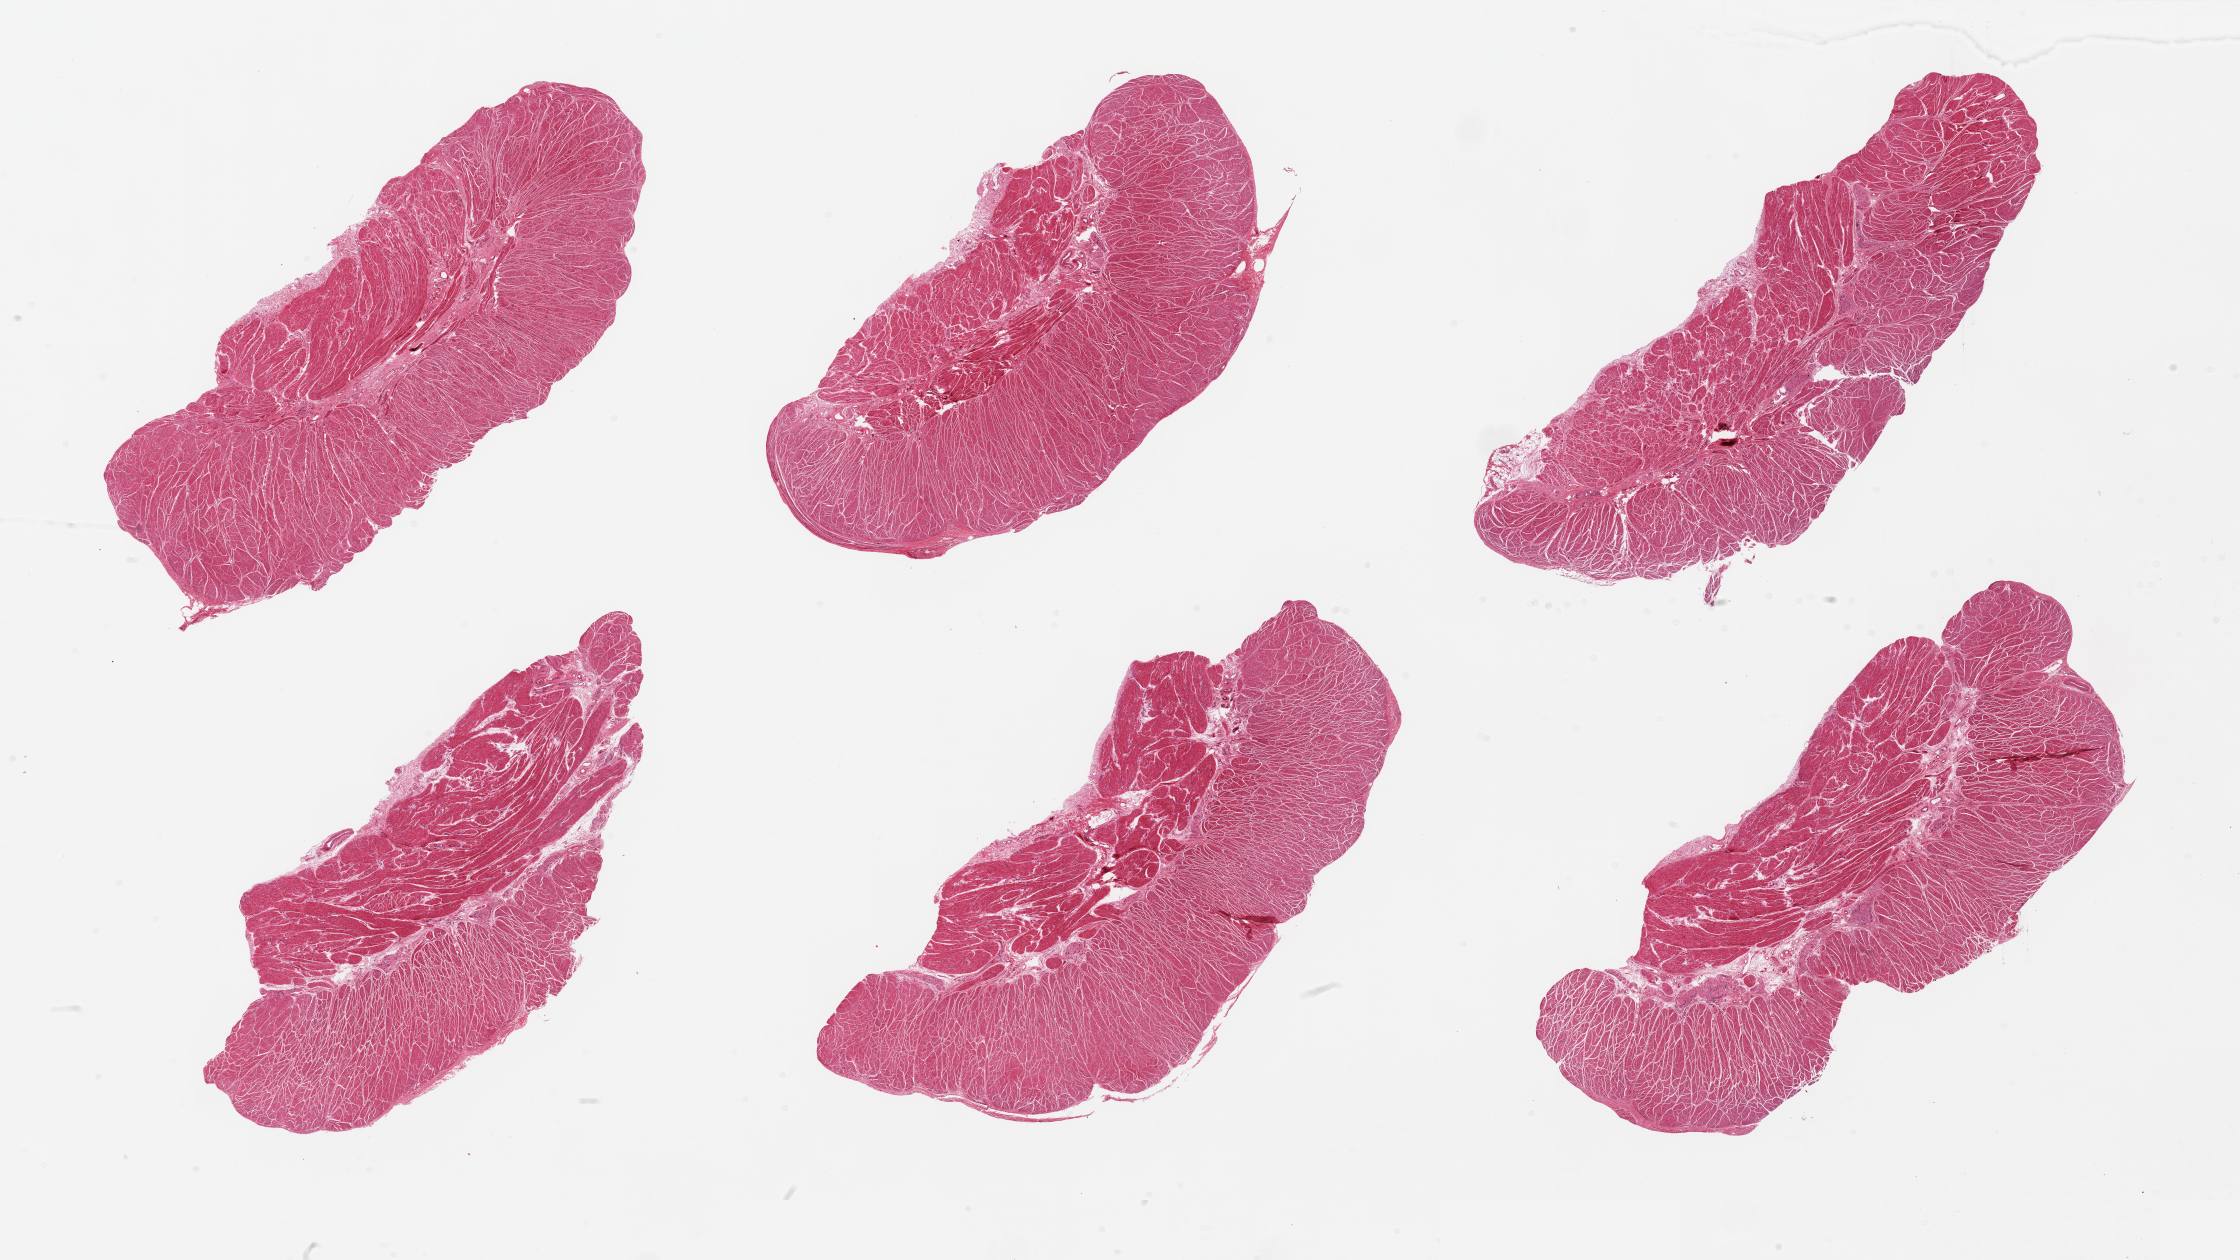
Digitized hematoxylin and eosin (H&E)-stained section — whole scanned area (about 35.4 x 19.9 mm) shown as a low-resolution overview. PAXgene-fixed paraffin-embedded (PFPE) section. Target tissue: esophageal muscle. Tissue donor sample. Donor sex: female.
Review note (as recorded): 6 pieces, all muscularis, good specimens.